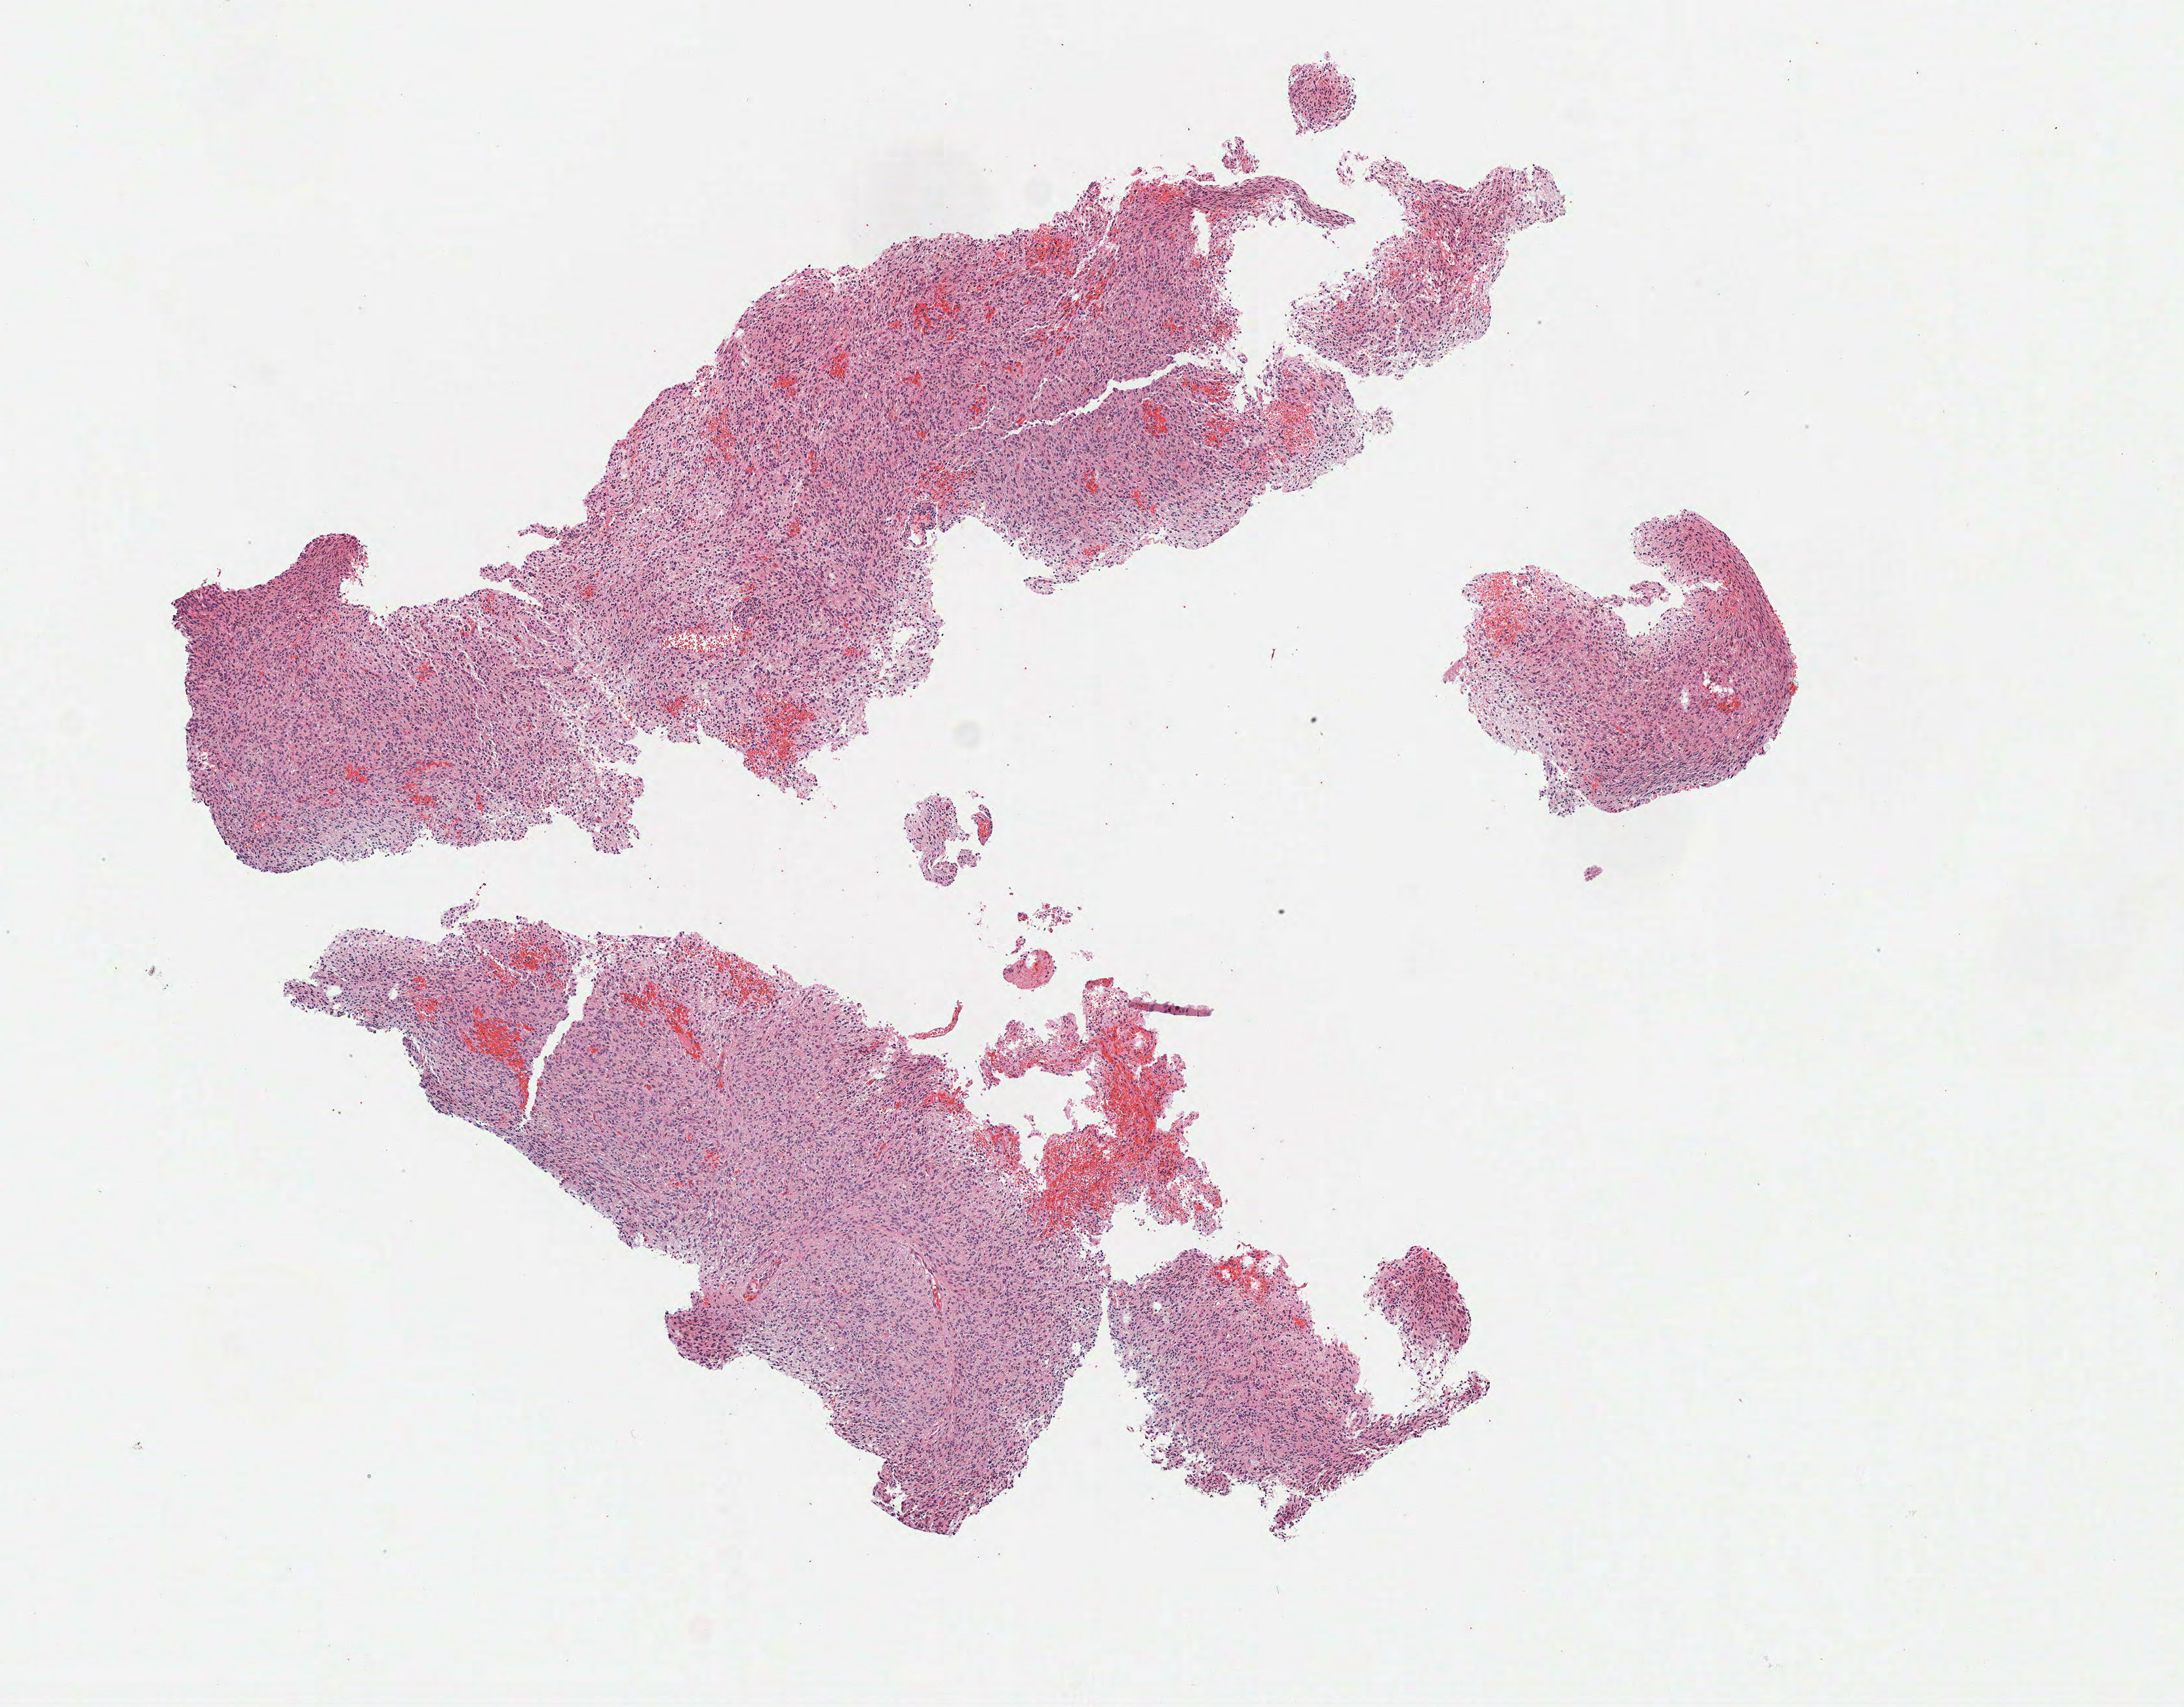
Whole-slide histology image, H&E-stained, low-resolution overview of the scanned area, about 6.6 x 5.1 mm. Frozen section. Brain, primary tumour sample. Female, age 34 years at initial diagnosis. Histologic grade: G3 (poorly differentiated). Composition of this section per pathologist review: tumour cells 100%, tumour nuclei 80%, normal cells 0%, stromal cells 0%, necrosis 0%.
• pathologic diagnosis: Astrocytoma, anaplastic
• laterality: right